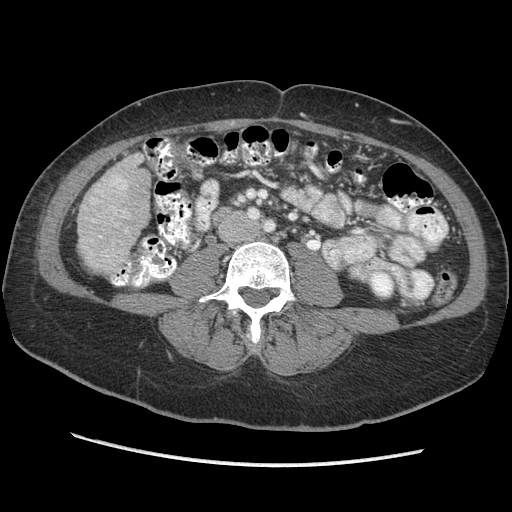
Contrast-enhanced abdominal CT (liver protocol), one axial slice; position 88 of 170 along the scan axis; reconstruction kernel STANDARD; soft-tissue window (W 400 / L 40 HU); 2.5 mm slice thickness; 512 × 512 image matrix, field of view 360 × 360 mm. Case-level facts recorded for this patient, not image findings: diagnosis: hepatocellular carcinoma (patient treated with transarterial chemoembolisation; whether this scan precedes or follows treatment is not stated here); TNM stage (as recorded): Stage-II; Child-Pugh class: A; tumour differentiation: no biopsy; tumour nodularity: multinodular.
Structures marked on this image (semi-automatic segmentation, software-assisted and operator-edited):
- liver parenchyma outside the tumour (the mass and vessels are separate outlines, so this box may not span the whole liver): bounding box <78,155,150,274> (left, top, right, bottom; pixels)
- liver vessels: <112,178,127,189>